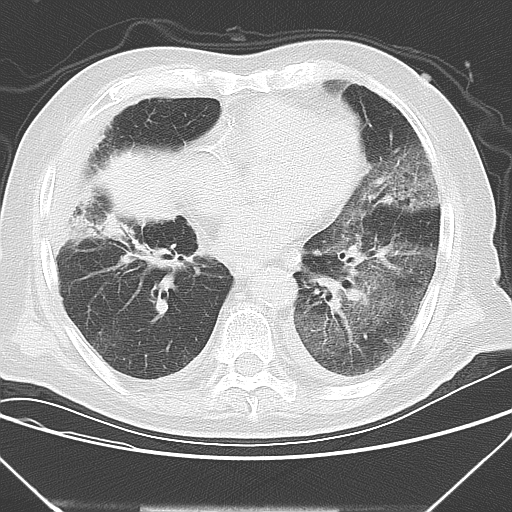
Chest CT, one axial slice; position 12 of 43 along the scan axis; lung window (W 1500 / L -600 HU); 5 mm slice thickness; 512 × 512 image matrix. Male patient, age 85 years. From the clinical record (not read from this slice): clinical TNM (as recorded): T4 N3 M2.
Outlined on this slice (bounding box drawn by a radiologist):
- lung tumour (recorded histology: squamous cell carcinoma): box from (x=90, y=136) to (x=187, y=248) px